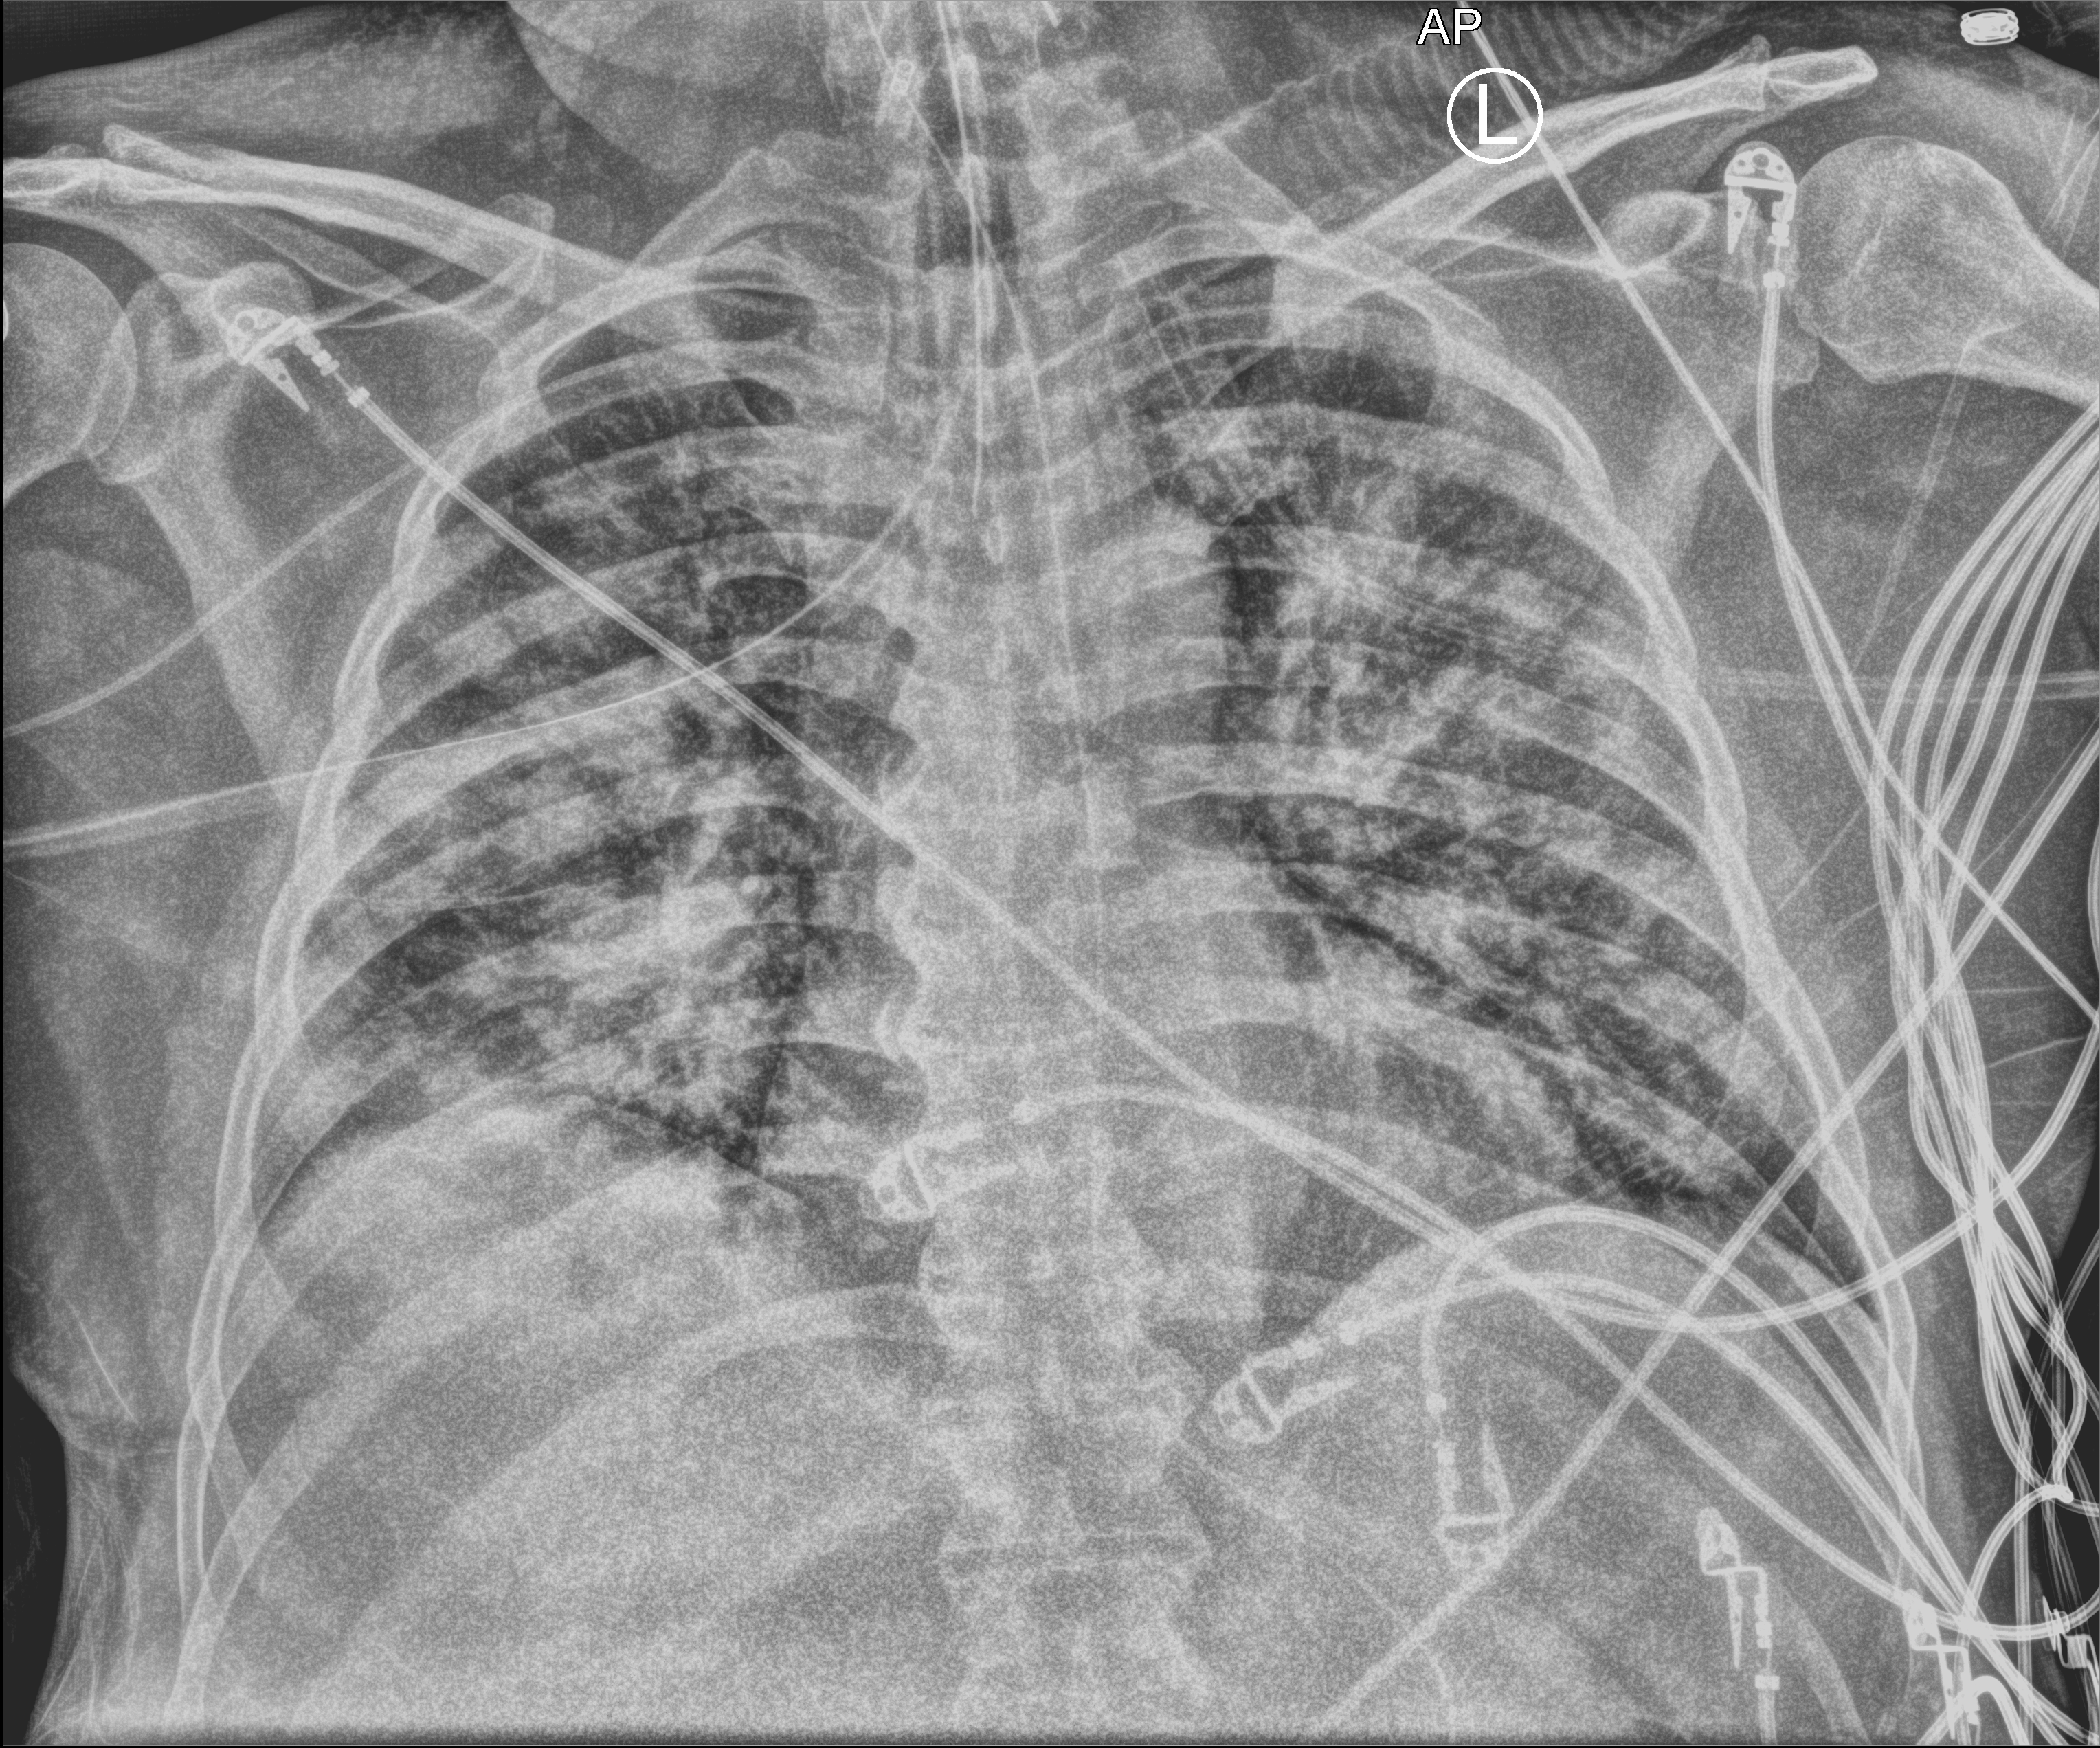
Bedside chest radiograph (computed radiography), anteroposterior (AP) projection. Patient hospitalised with COVID-19; male, aged 18–59 years.
Admission-level facts for this patient (not findings on this image; timing relative to this image not recorded): chronic kidney disease (admission record): no; admitted to intensive care during this hospital stay: yes; length of hospital stay: 26 days.